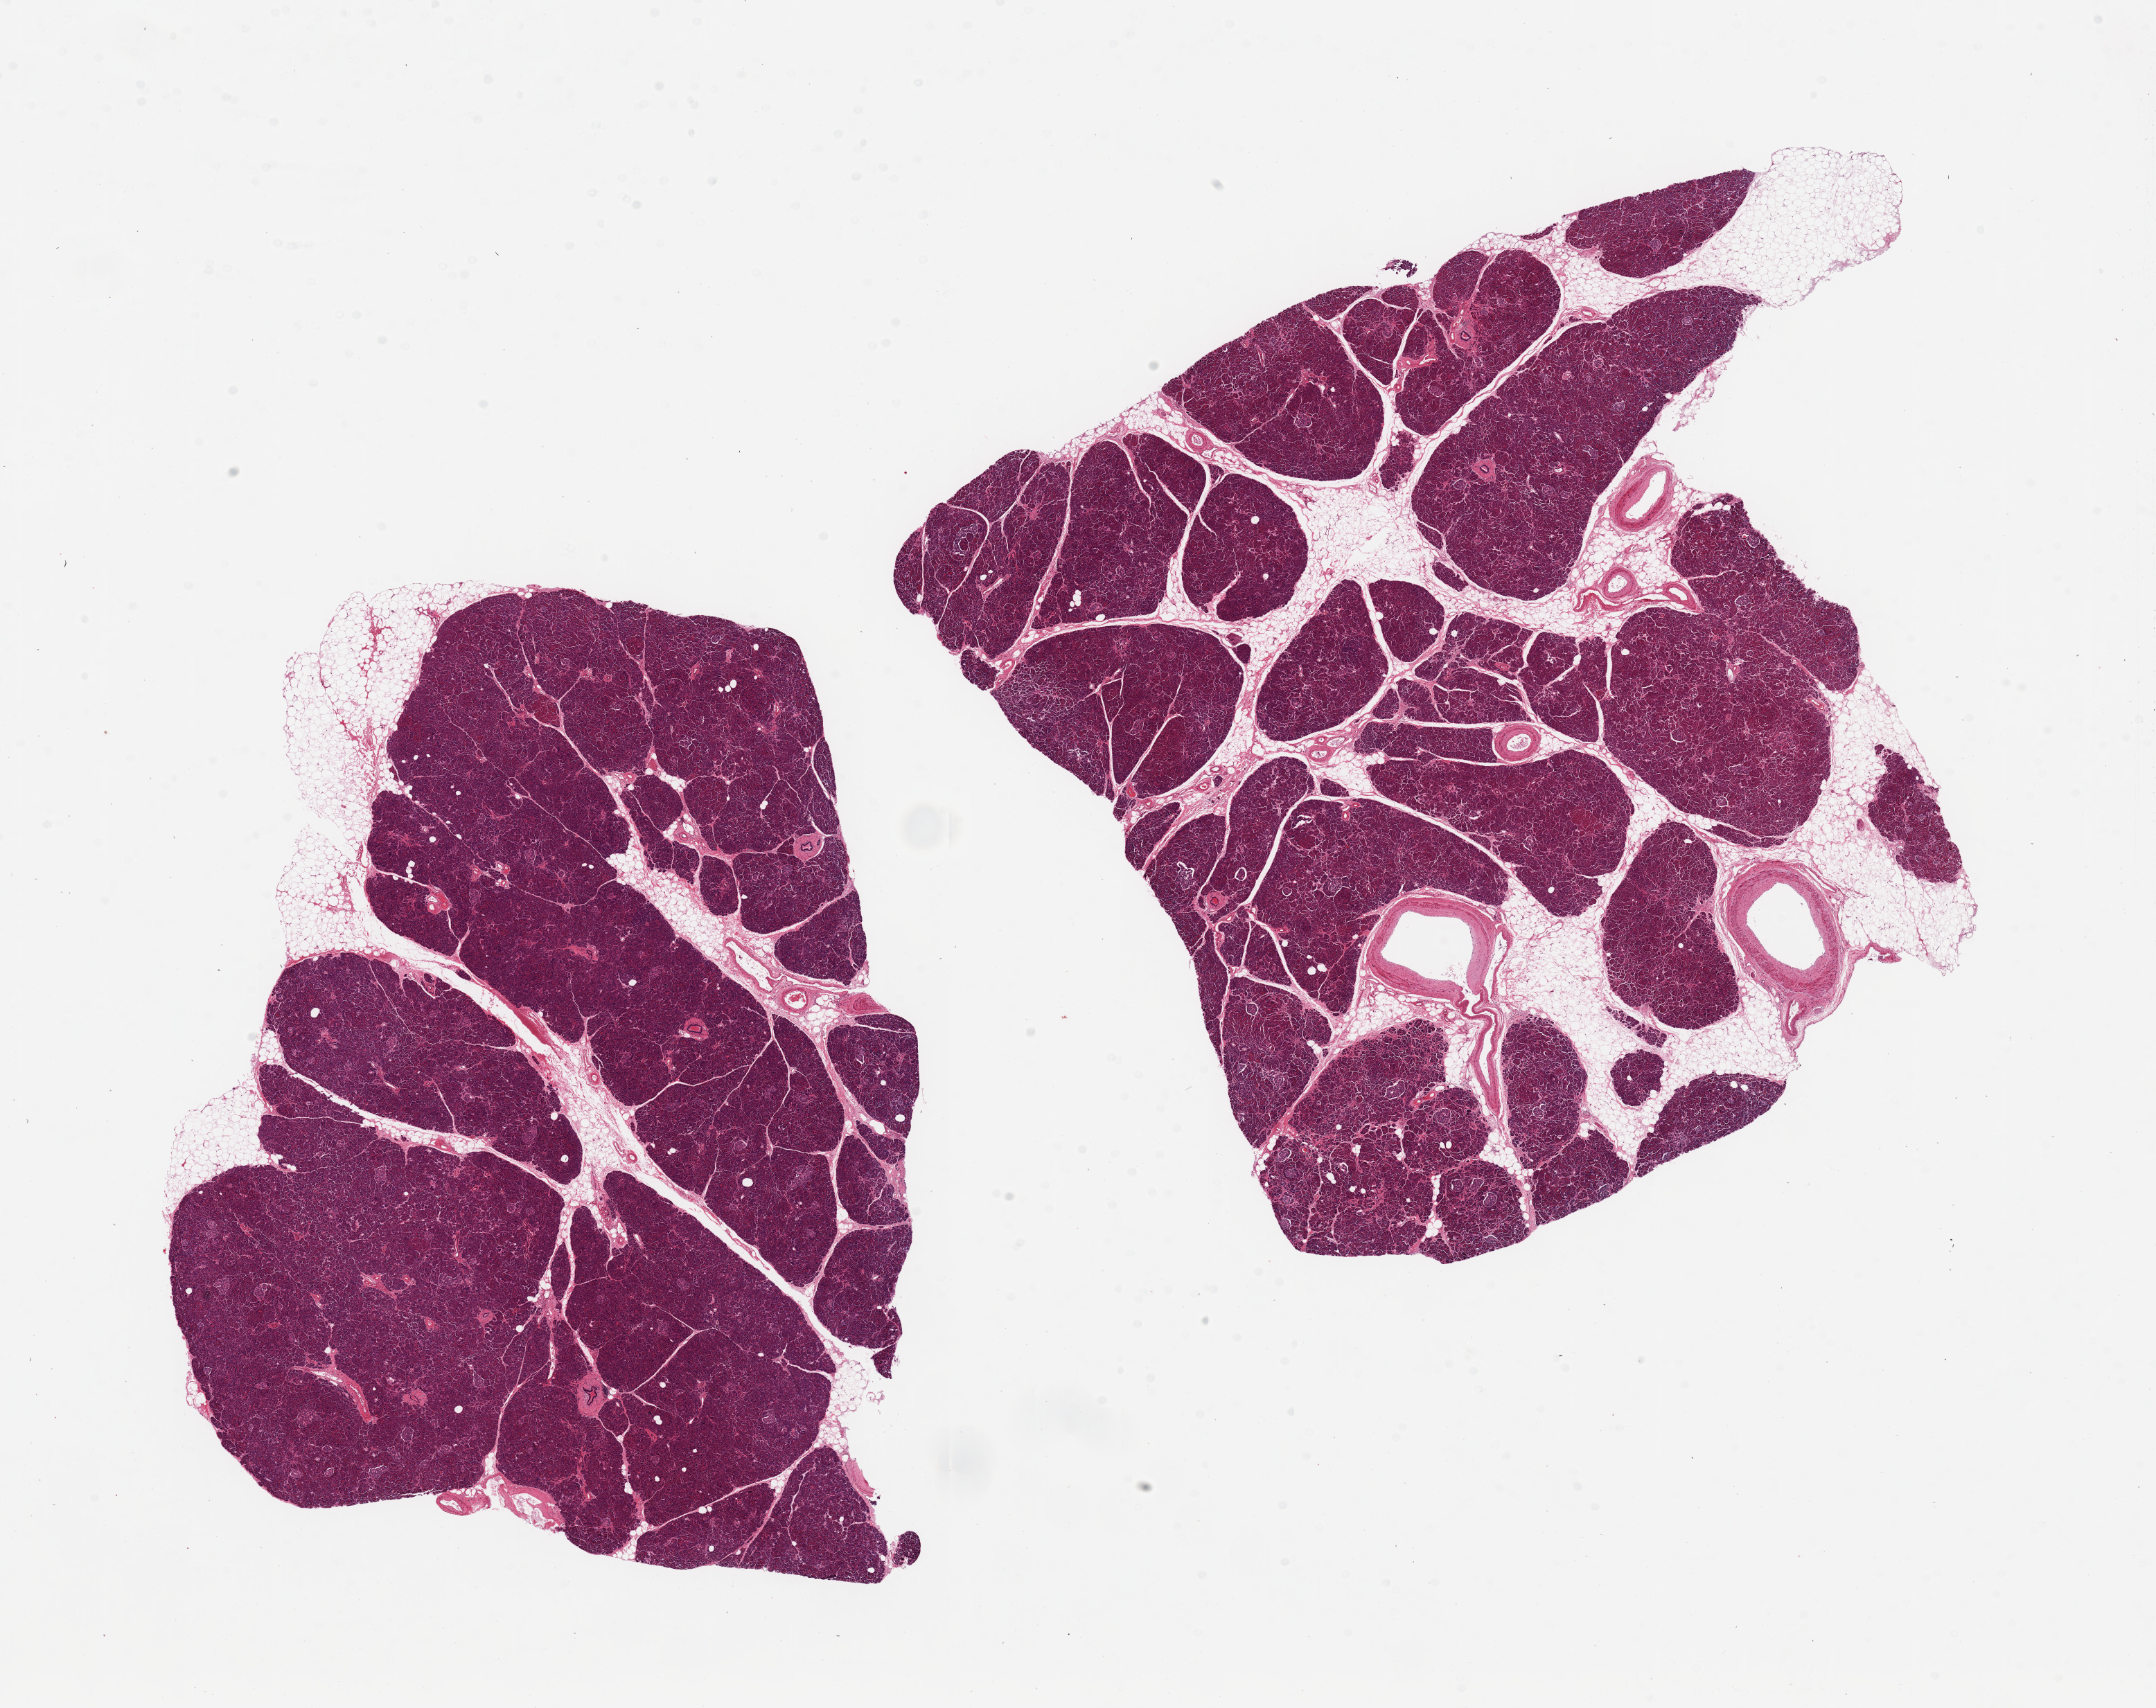
Whole-slide image, haematoxylin and eosin stain, low-resolution overview of the scanned area, about 24.6 x 19.5 mm, PAXgene-fixed, paraffin-embedded tissue, section of pancreas (target tissue), donor tissue sample.
Reviewer comment on this tissue sample: 2 pieces, ~11x9mm, well preserved, ~20% interstitital and adherent fat; Islets well- visualized.